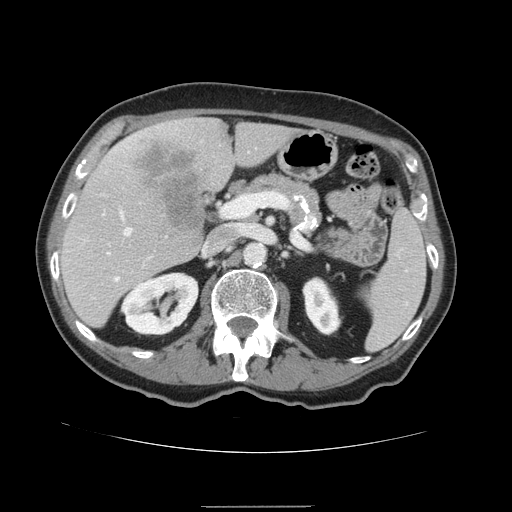
Contrast-enhanced abdominal CT, one axial slice. Position 82 of 168 along the scan axis. Intravenous contrast given. Soft-tissue window (W 400 / L 40 HU). 512 × 512 image matrix, field of view 386 × 386 mm. Male patient, age 74 years. Case-level facts recorded for this patient, not image findings: diagnosis: colorectal cancer liver metastases, imaged before liver resection; multiple liver metastases: no; largest metastasis: 14.5 cm; chemotherapy before resection: no.
Annotated regions visible in this slice (expert manual segmentation):
- hepatic veins: bounding box <116,211,132,279> (left, top, right, bottom; pixels)
- liver: <60,117,300,329>
- planned liver remnant (the part of the liver to remain after resection): <60,123,300,329>
- portal vein (with intrahepatic branches): <106,199,240,269>
- liver metastasis: <131,139,207,233>